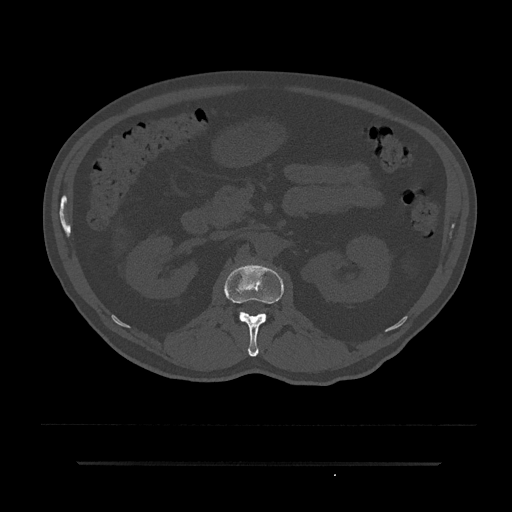
CT including the spine, one axial slice. Slice 125 of 797 in the series (ordered by position). Reconstruction kernel Br40s/3. Bone window (W 1800 / L 400 HU). 0.5 mm slice thickness. 512 × 512 image matrix, field of view 464 × 464 mm. Patient: male, 59 years. Case-level facts recorded for this patient, not image findings: primary cancer: bile ducts; vertebrae with lytic lesions (as recorded): T10.
Outlined on this slice (semi-automatically segmented with operator editing):
- L1 vertebra: box from (x=224, y=264) to (x=284, y=357) px